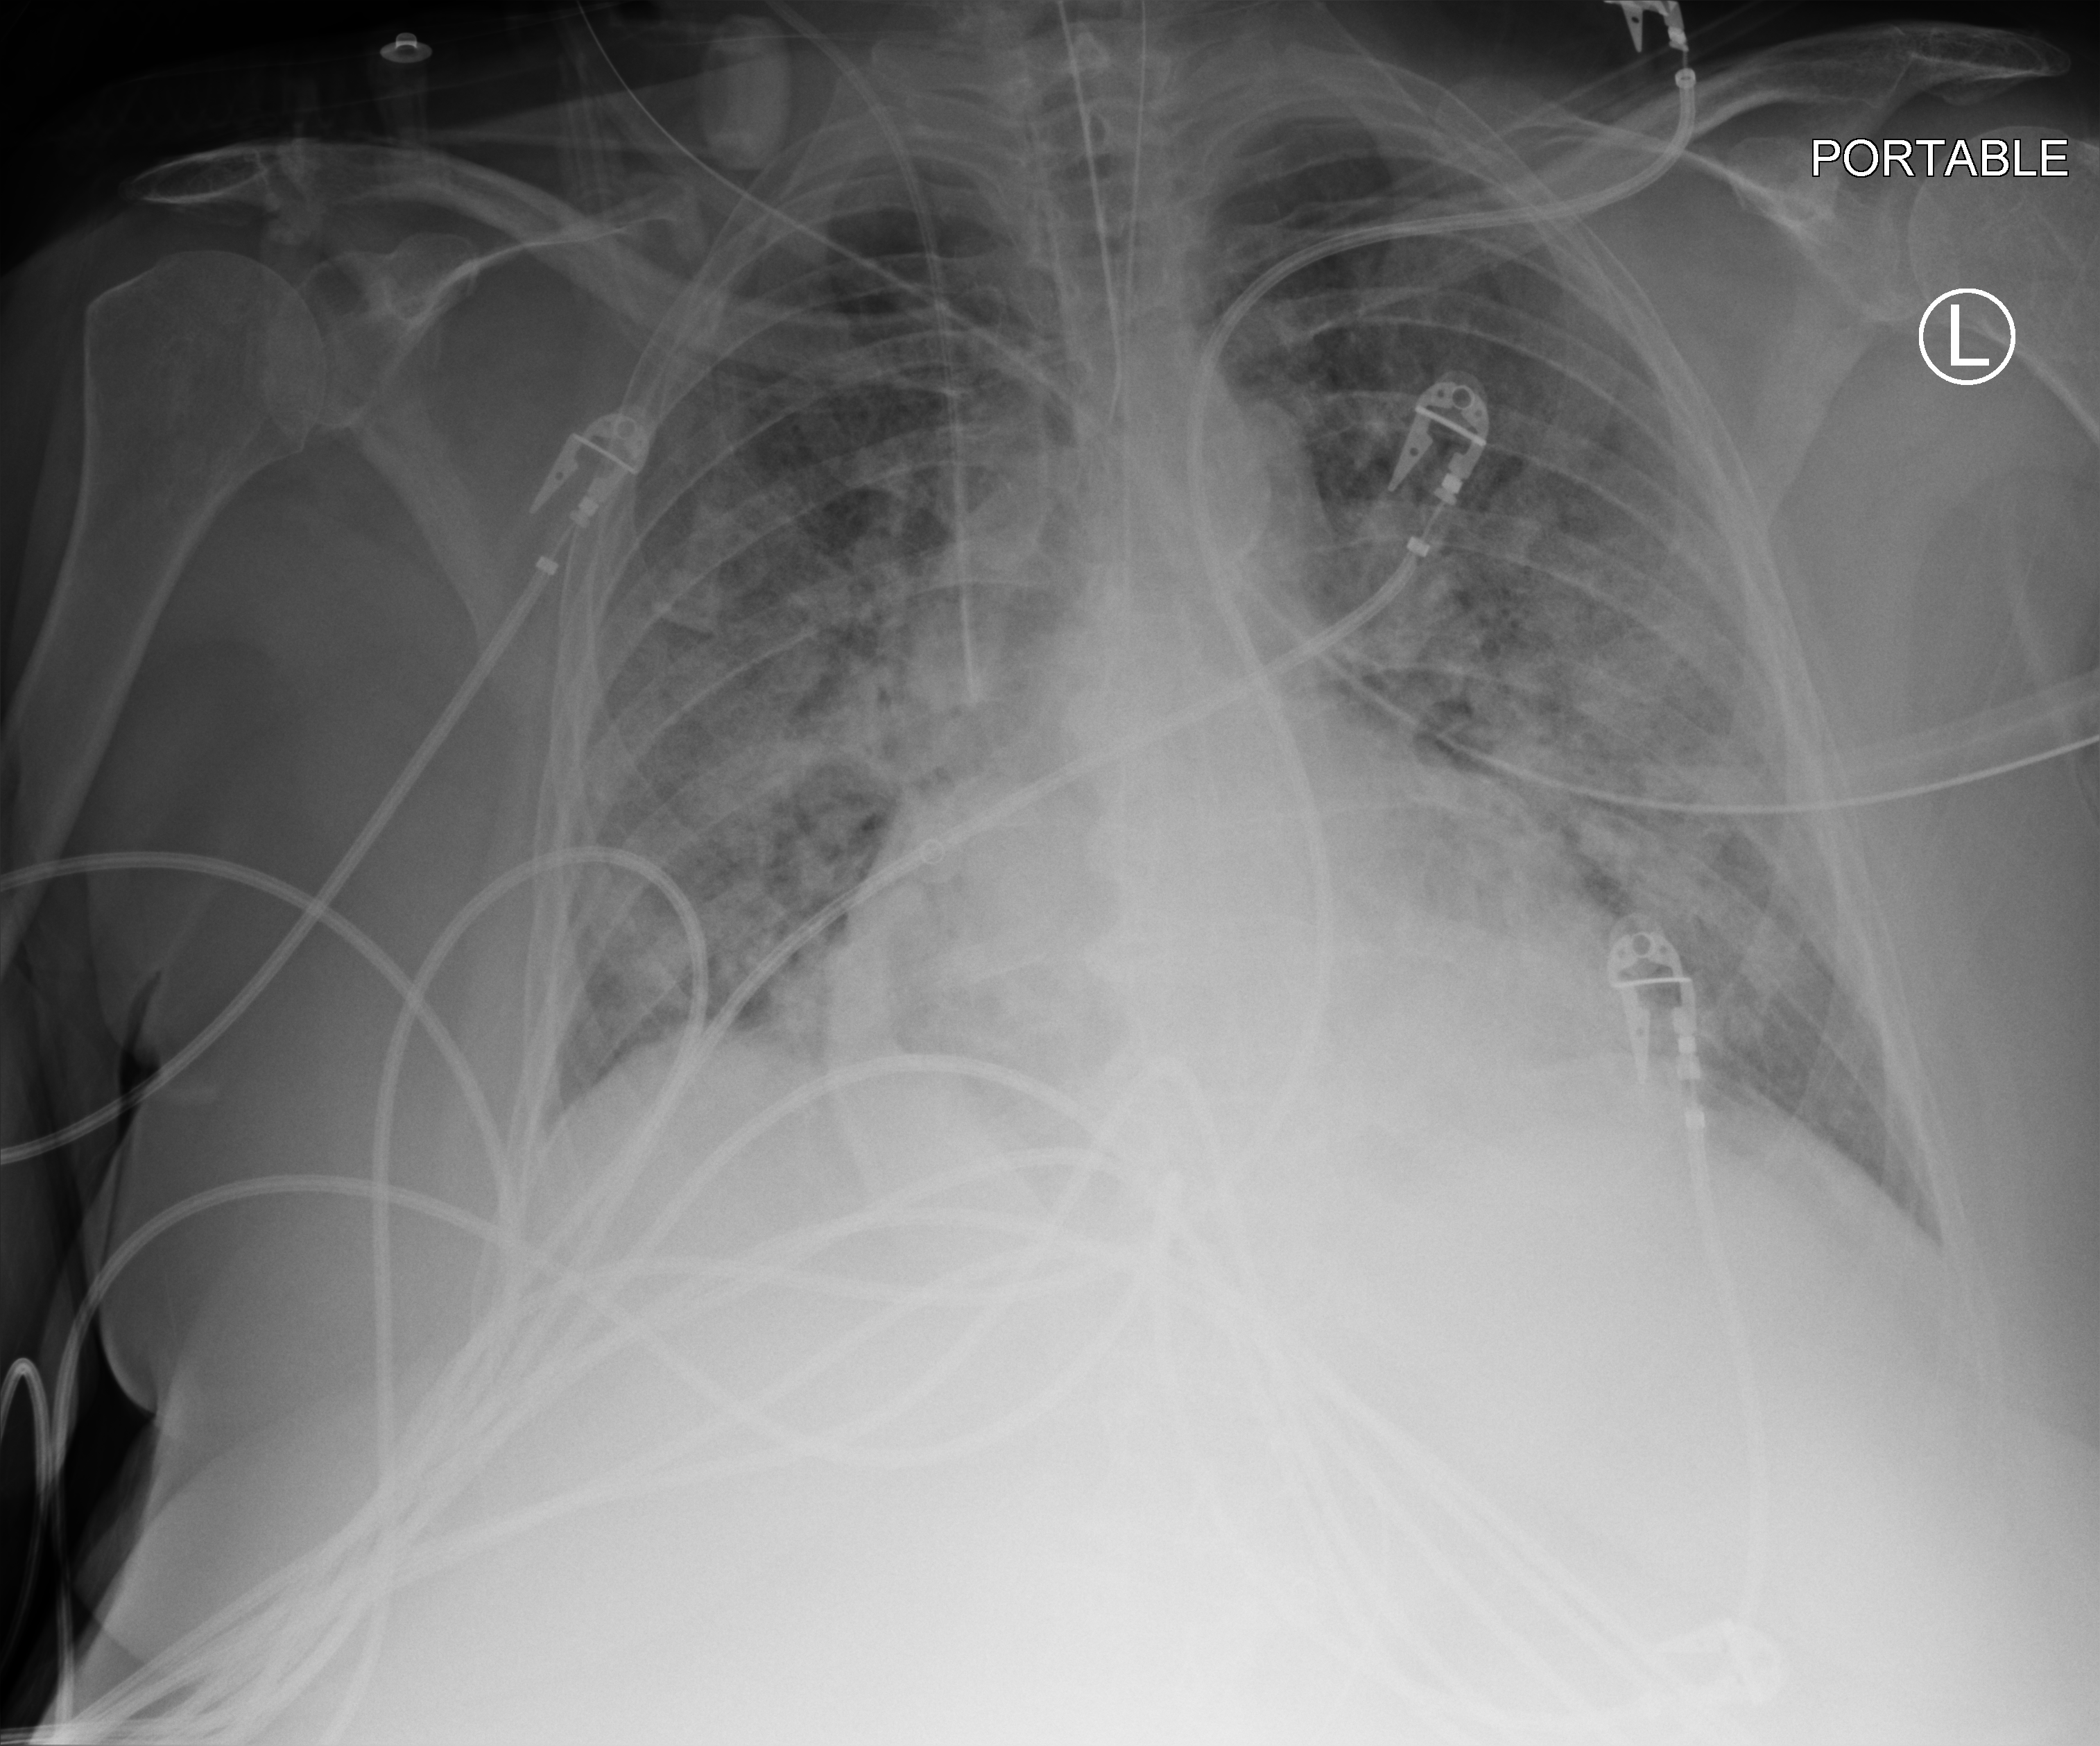
Bedside chest radiograph (computed radiography); anteroposterior (AP) projection. Patient hospitalised with COVID-19; female, aged 75–90 years.
Admission-level facts for this patient (not findings on this image; timing relative to this image not recorded): length of hospital stay: 31 days.